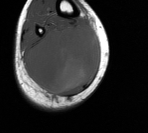
MRI of an extremity soft-tissue mass, one axial slice; slice 44 of 76 in the series (ordered by position); MR volume resampled by the dataset authors to the PET/CT grid (not the native acquisition matrix); 3.27 mm slice thickness; 148 × 133 image matrix. Male patient. Case-level facts recorded for this patient, not image findings: histological type: liposarcoma - round cell; grade: high; site of the primary tumour: right calf.
Structures marked on this image (expert contour drawn on MRI and transferred to this co-registered scan by the dataset authors):
- gross tumour volume (mass): bounding box <26,26,101,93> (left, top, right, bottom; pixels)